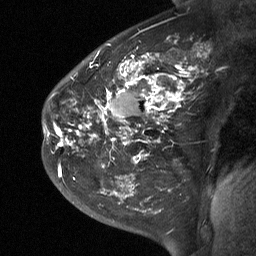
Breast MRI (dynamic contrast-enhanced), one sagittal slice. Position 39 of 64 along the scan axis. Dynamic contrast-enhanced study with each time point stored as its own series, time point 2 of 3 at this slice position (early post-contrast, ordered by acquisition time). 1.5 T. TE 4.8 ms, TR 27 ms. 2 mm slice thickness. 256 × 256 image matrix, field of view 200 × 200 mm. Patient: female, 42 years. From the clinical record (not read from this slice): setting: breast cancer imaged before/during neoadjuvant chemotherapy; receptor status: triple-negative.
Annotated regions visible in this slice (semi-automatically segmented with operator editing):
- analysis volume of interest (the breast-tissue region the enhancement analysis was run in; not a lesion): bounding box <43,29,202,190> (left, top, right, bottom; pixels)
- tumour enhancement mask (voxels above the 90 % enhancement threshold inside the analysis volume of interest): <45,61,193,177>